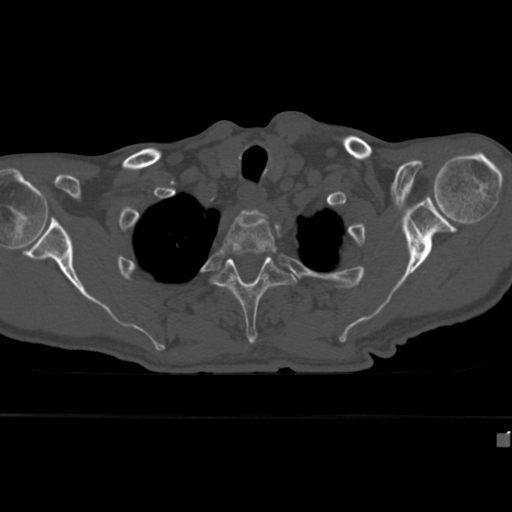
CT including the spine, one axial slice; slice 336 of 430 in the series (ordered by position); 120 kVp; bone window (W 1800 / L 400 HU); 1.5 mm slice thickness; 512 × 512 image matrix, field of view 337 × 337 mm. Patient: male, 64 years. Case-level facts recorded for this patient, not image findings: primary cancer: uterus; vertebrae with lytic lesions (as recorded): T1, T4, T5, T7, L5.
Outlined on this slice (semi-automatically segmented with operator editing):
- T2 vertebra: bounding box (x1, y1, x2, y2) in pixels: (219, 214, 278, 258)
- T3 vertebra: (211, 254, 297, 345)